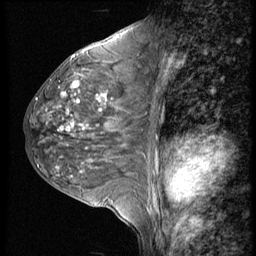
Breast MRI (dynamic contrast-enhanced), one sagittal slice. 4 images stored at this slice position (order not interpretable as contrast timing). 1.5 T. TE 4.2 ms, TR 9 ms. 256 × 256 image matrix, field of view 180 × 180 mm. Patient: female, 50 years. From the clinical record (not read from this slice): setting: breast cancer imaged before/during neoadjuvant chemotherapy; receptor status: triple-negative.
Outlined on this slice (semi-automatically segmented with operator editing):
- analysis volume of interest (the breast-tissue region the enhancement analysis was run in; not a lesion): bounding box [x1, y1, x2, y2] px = [23, 46, 148, 188]
- tumour enhancement mask (voxels above the 140 % enhancement threshold inside the analysis volume of interest): [36, 56, 107, 131]